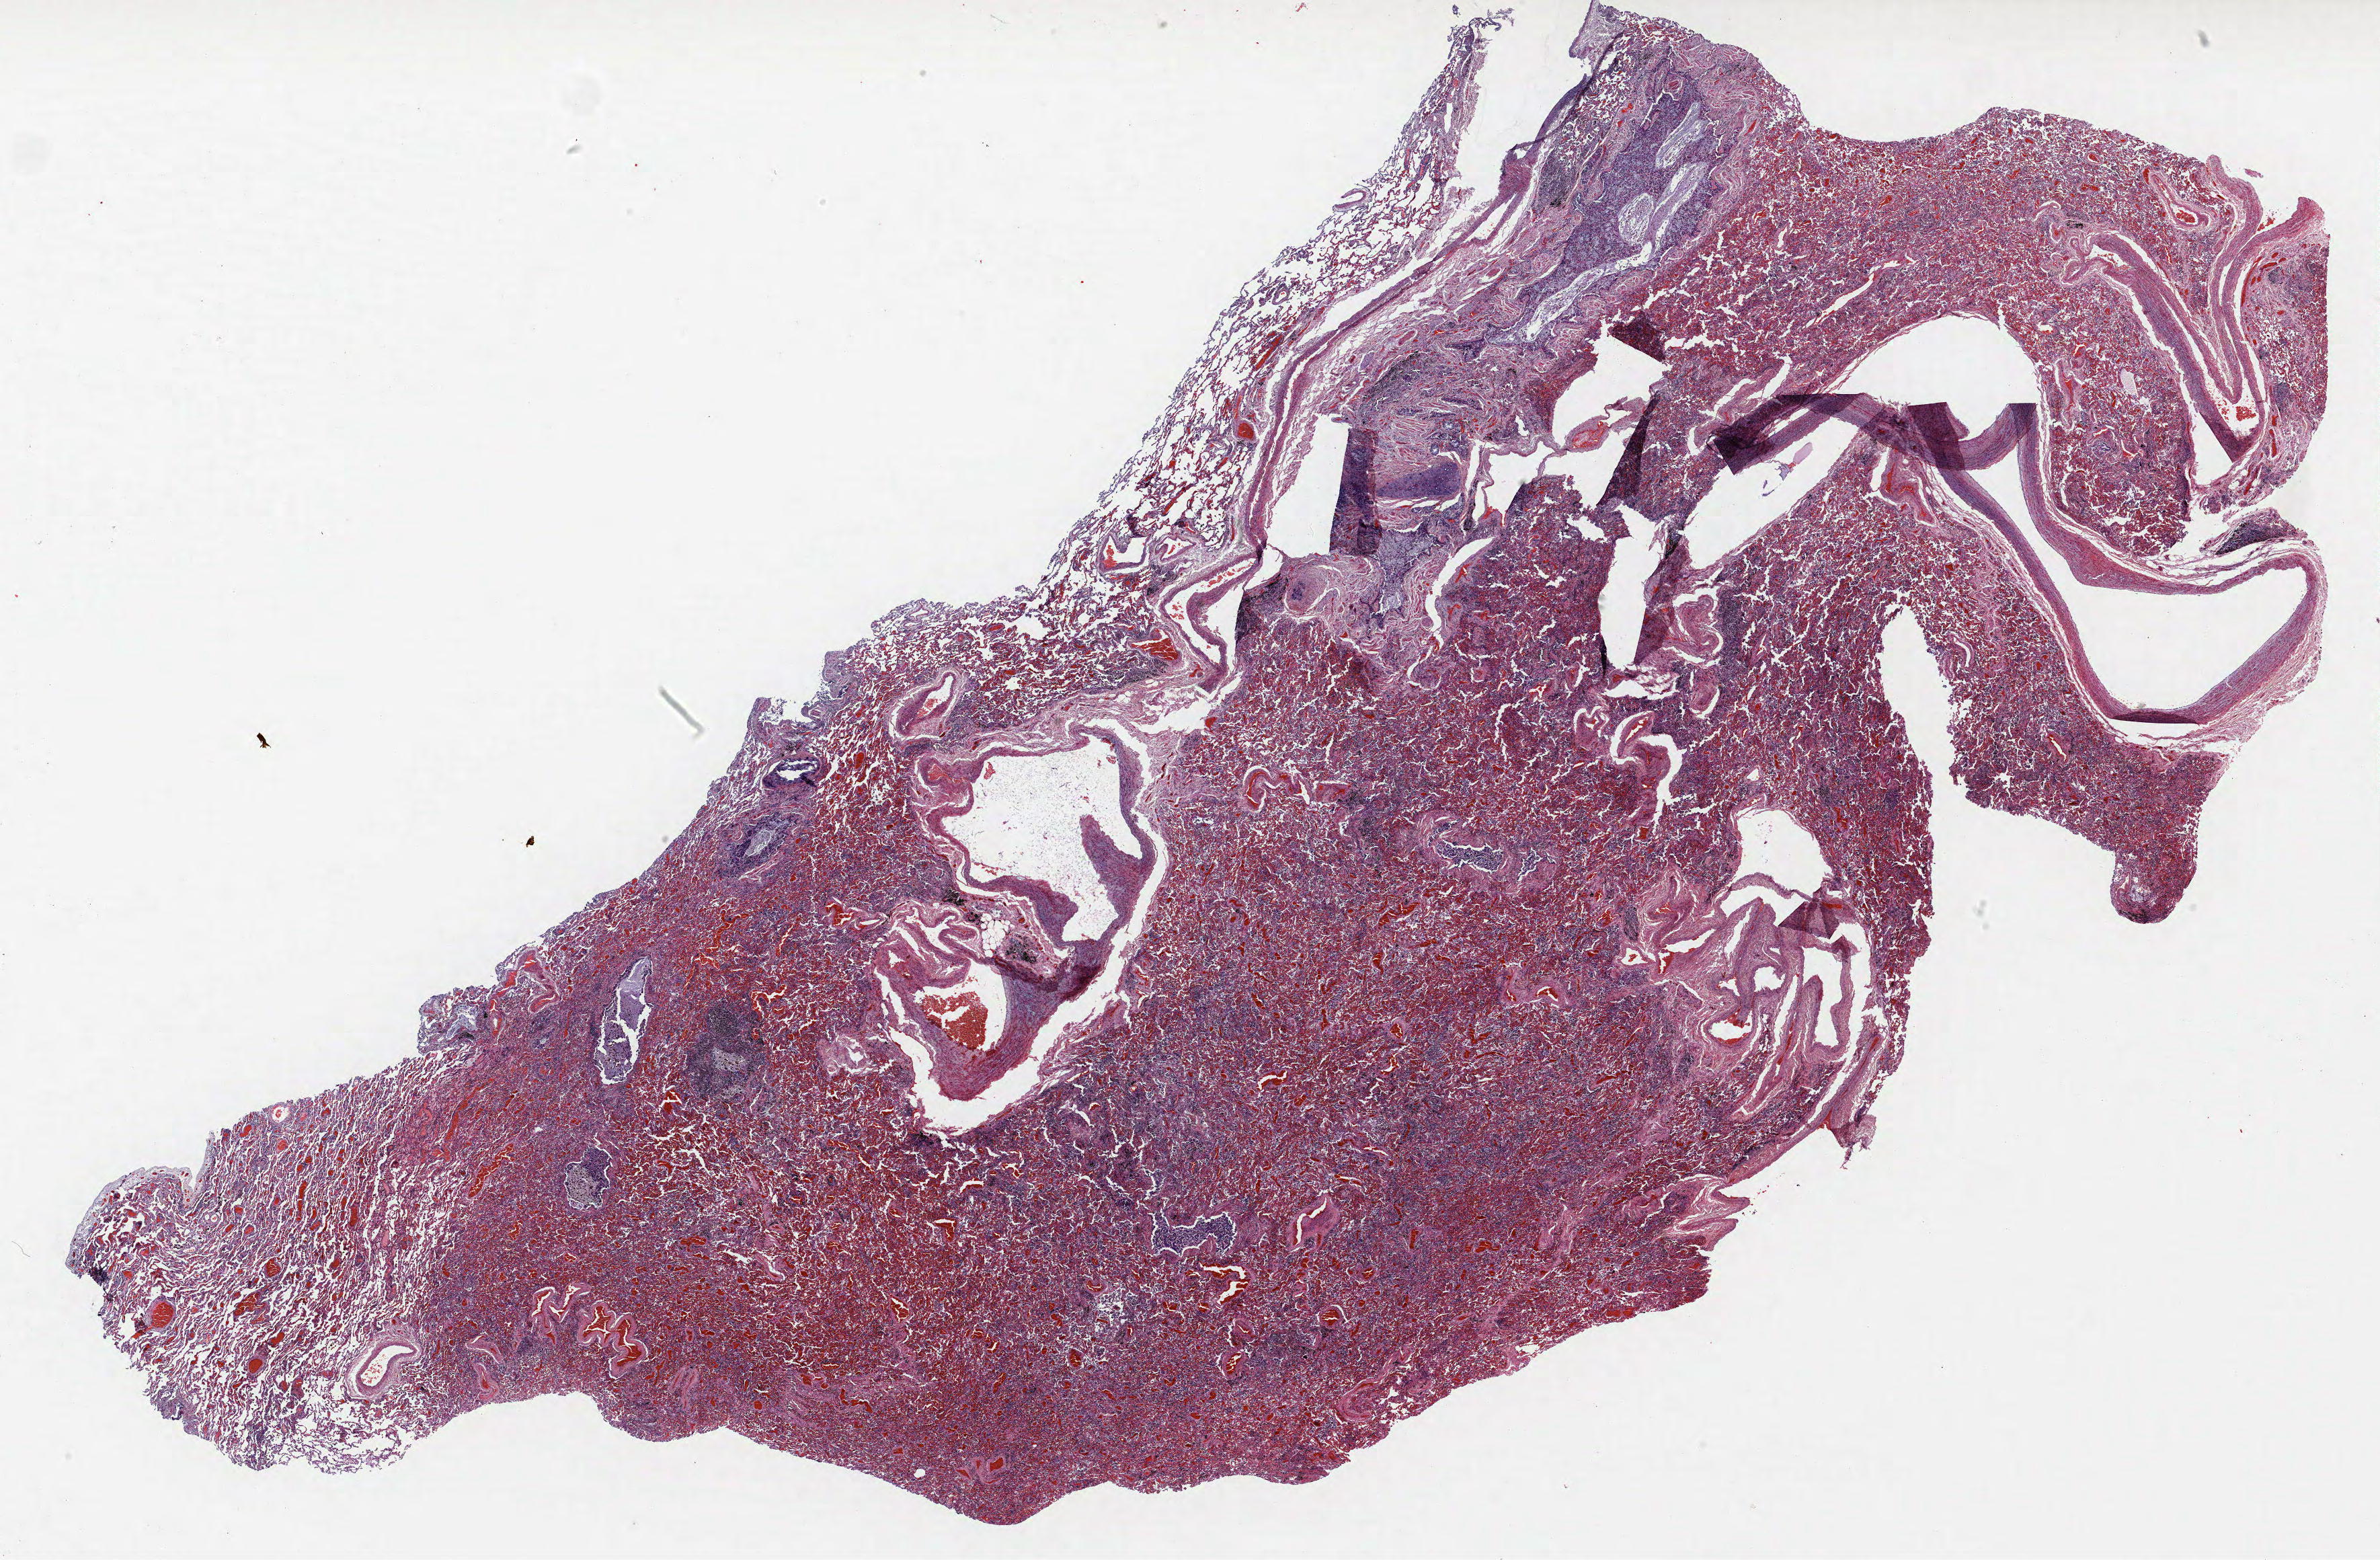
H&E whole-slide image, shown as a low-resolution overview of the whole scanned area (about 28.3 x 18.6 mm, from a 40x scan); formalin-fixed paraffin-embedded (FFPE) section; lung. Female, age 61 at enrolment. Grade: well differentiated (G1).
• stage (AJCC 6th edition): IIIB
• participant's lung-cancer diagnosis: Adenocarcinoma, NOS
• tumour size (pathology): 30 mm
• primary tumour location (clinical record): right upper lobe
• note: participant had 2 primary lung cancers recorded; fields above describe the first